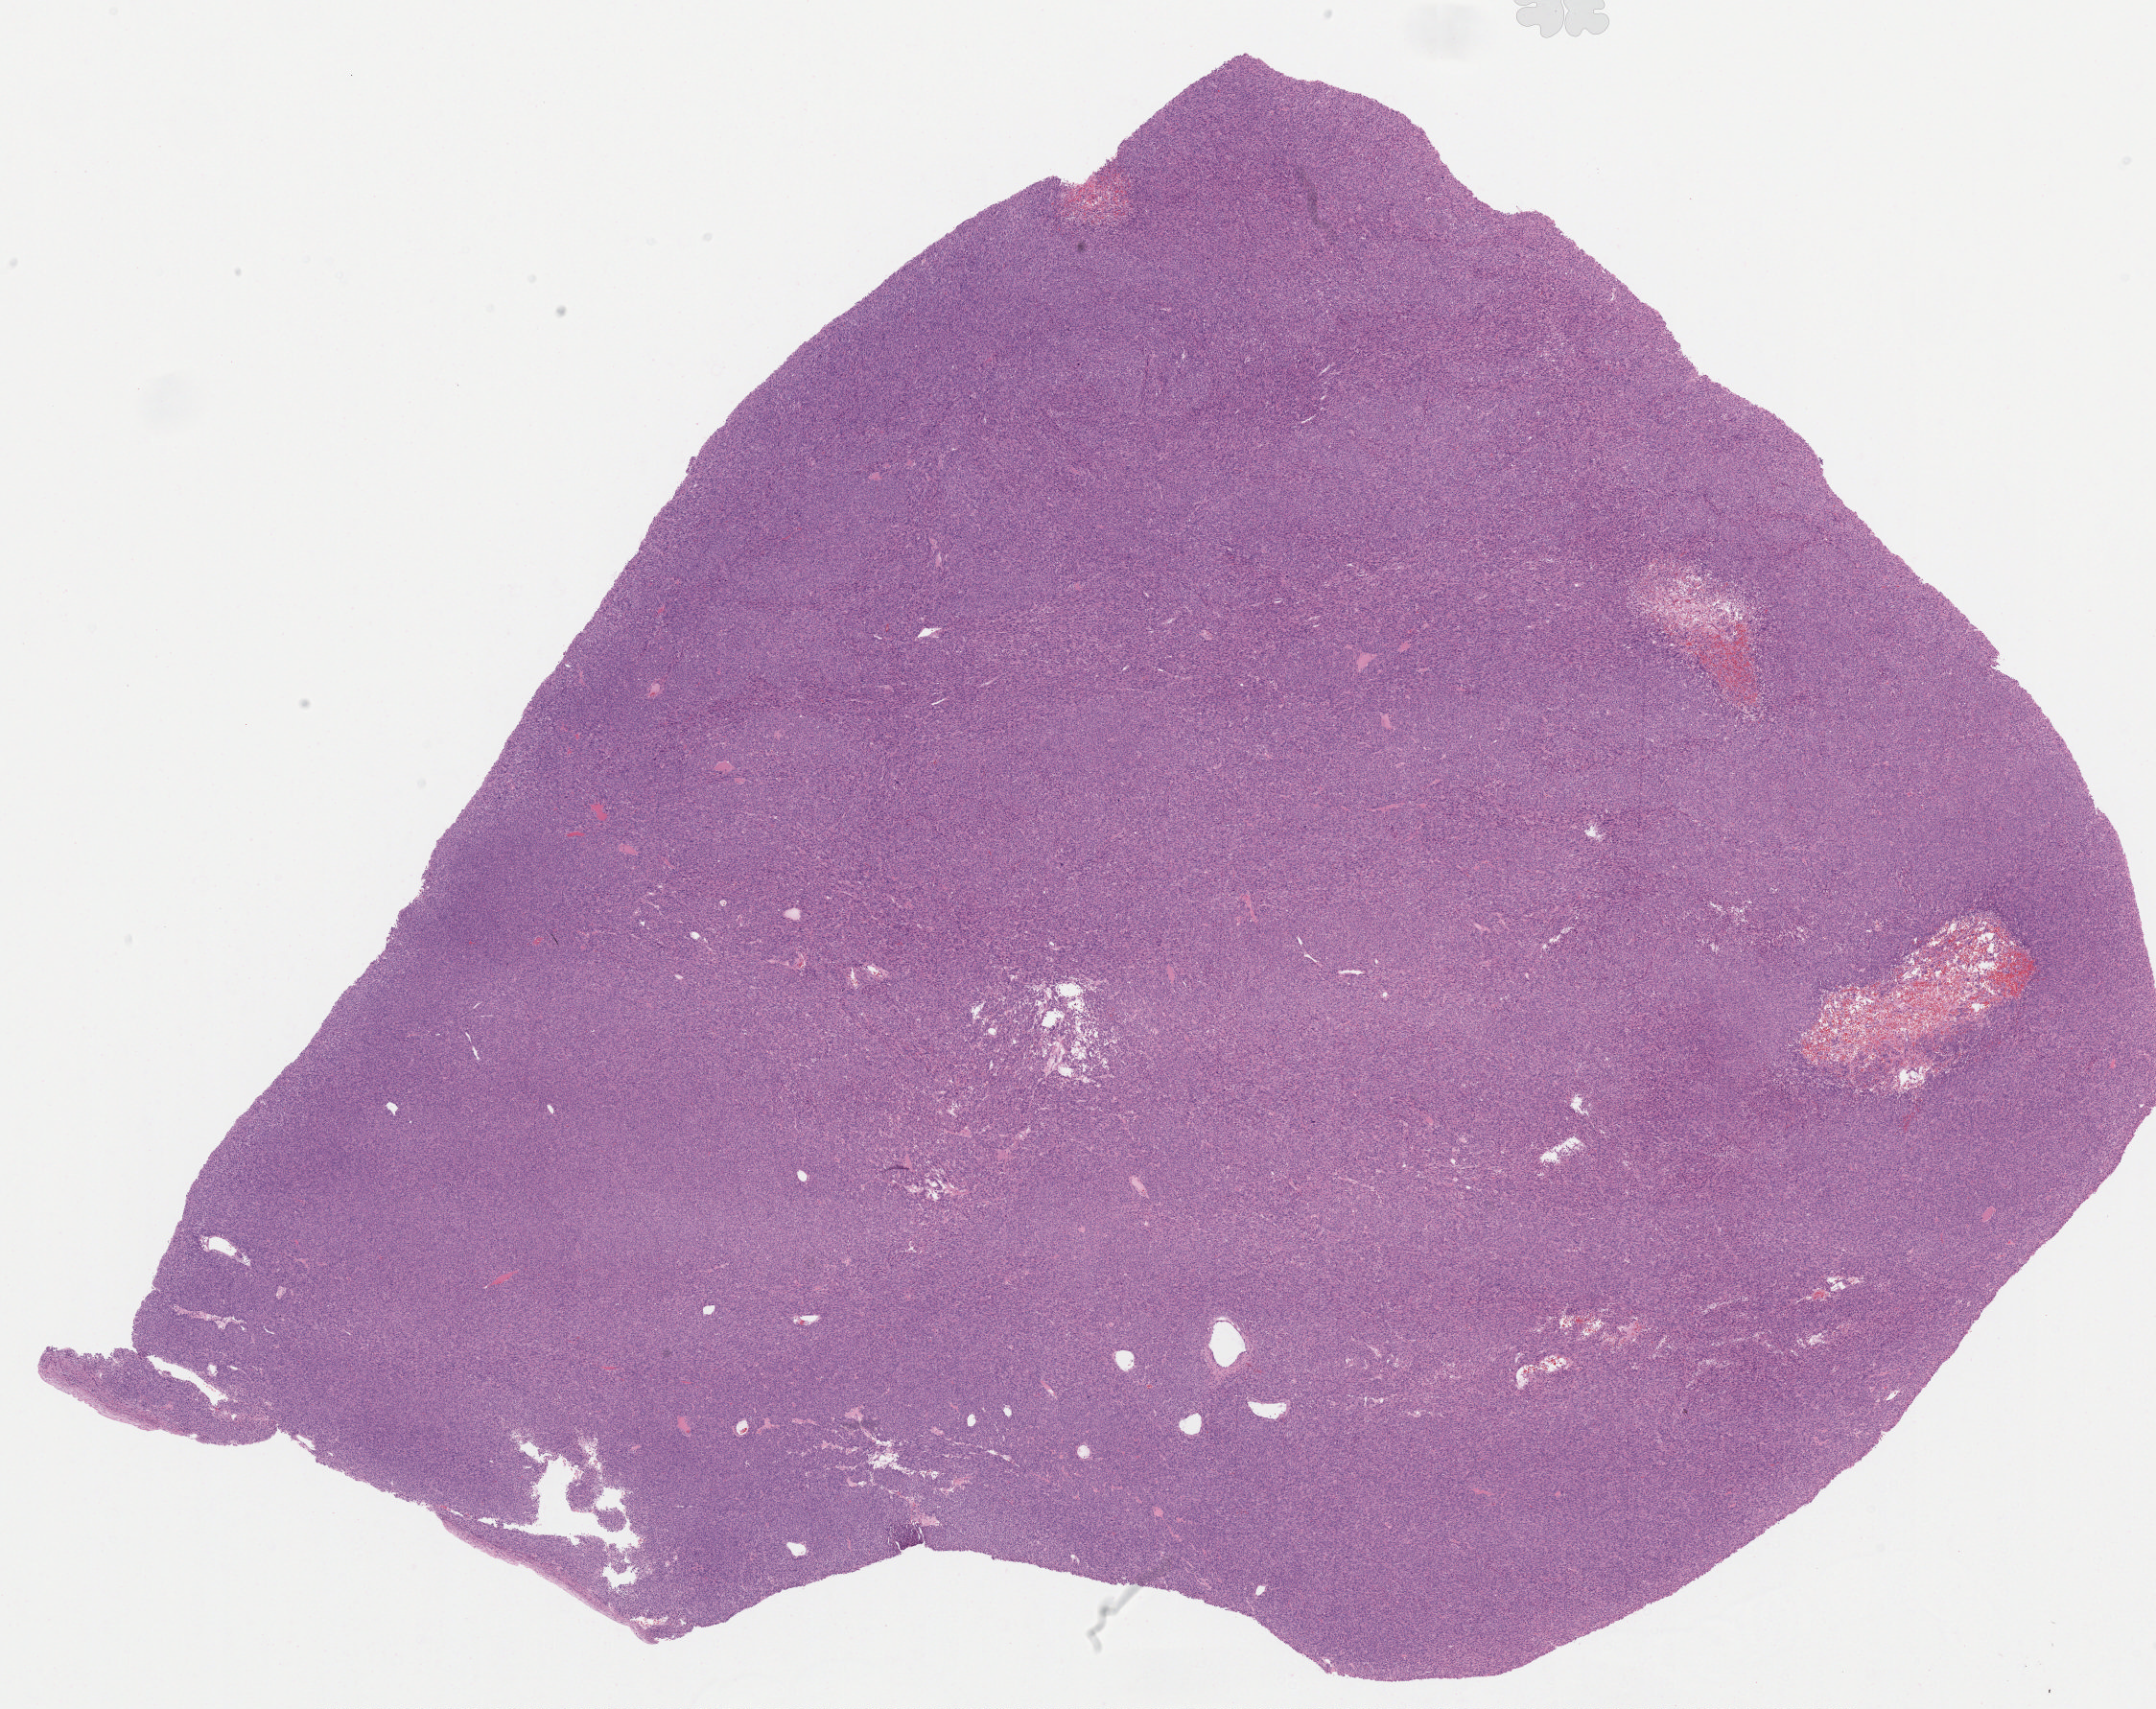
Digitized H&E tissue section (whole slide), whole scanned area (about 18.0 x 14.3 mm, acquisition: 20x scan) shown as a low-resolution overview. Formalin-fixed paraffin-embedded (FFPE) diagnostic section. Sample: primary tumour, uterus. Female, age 65 years at initial diagnosis.
Diagnosis: Leiomyosarcoma, NOS.